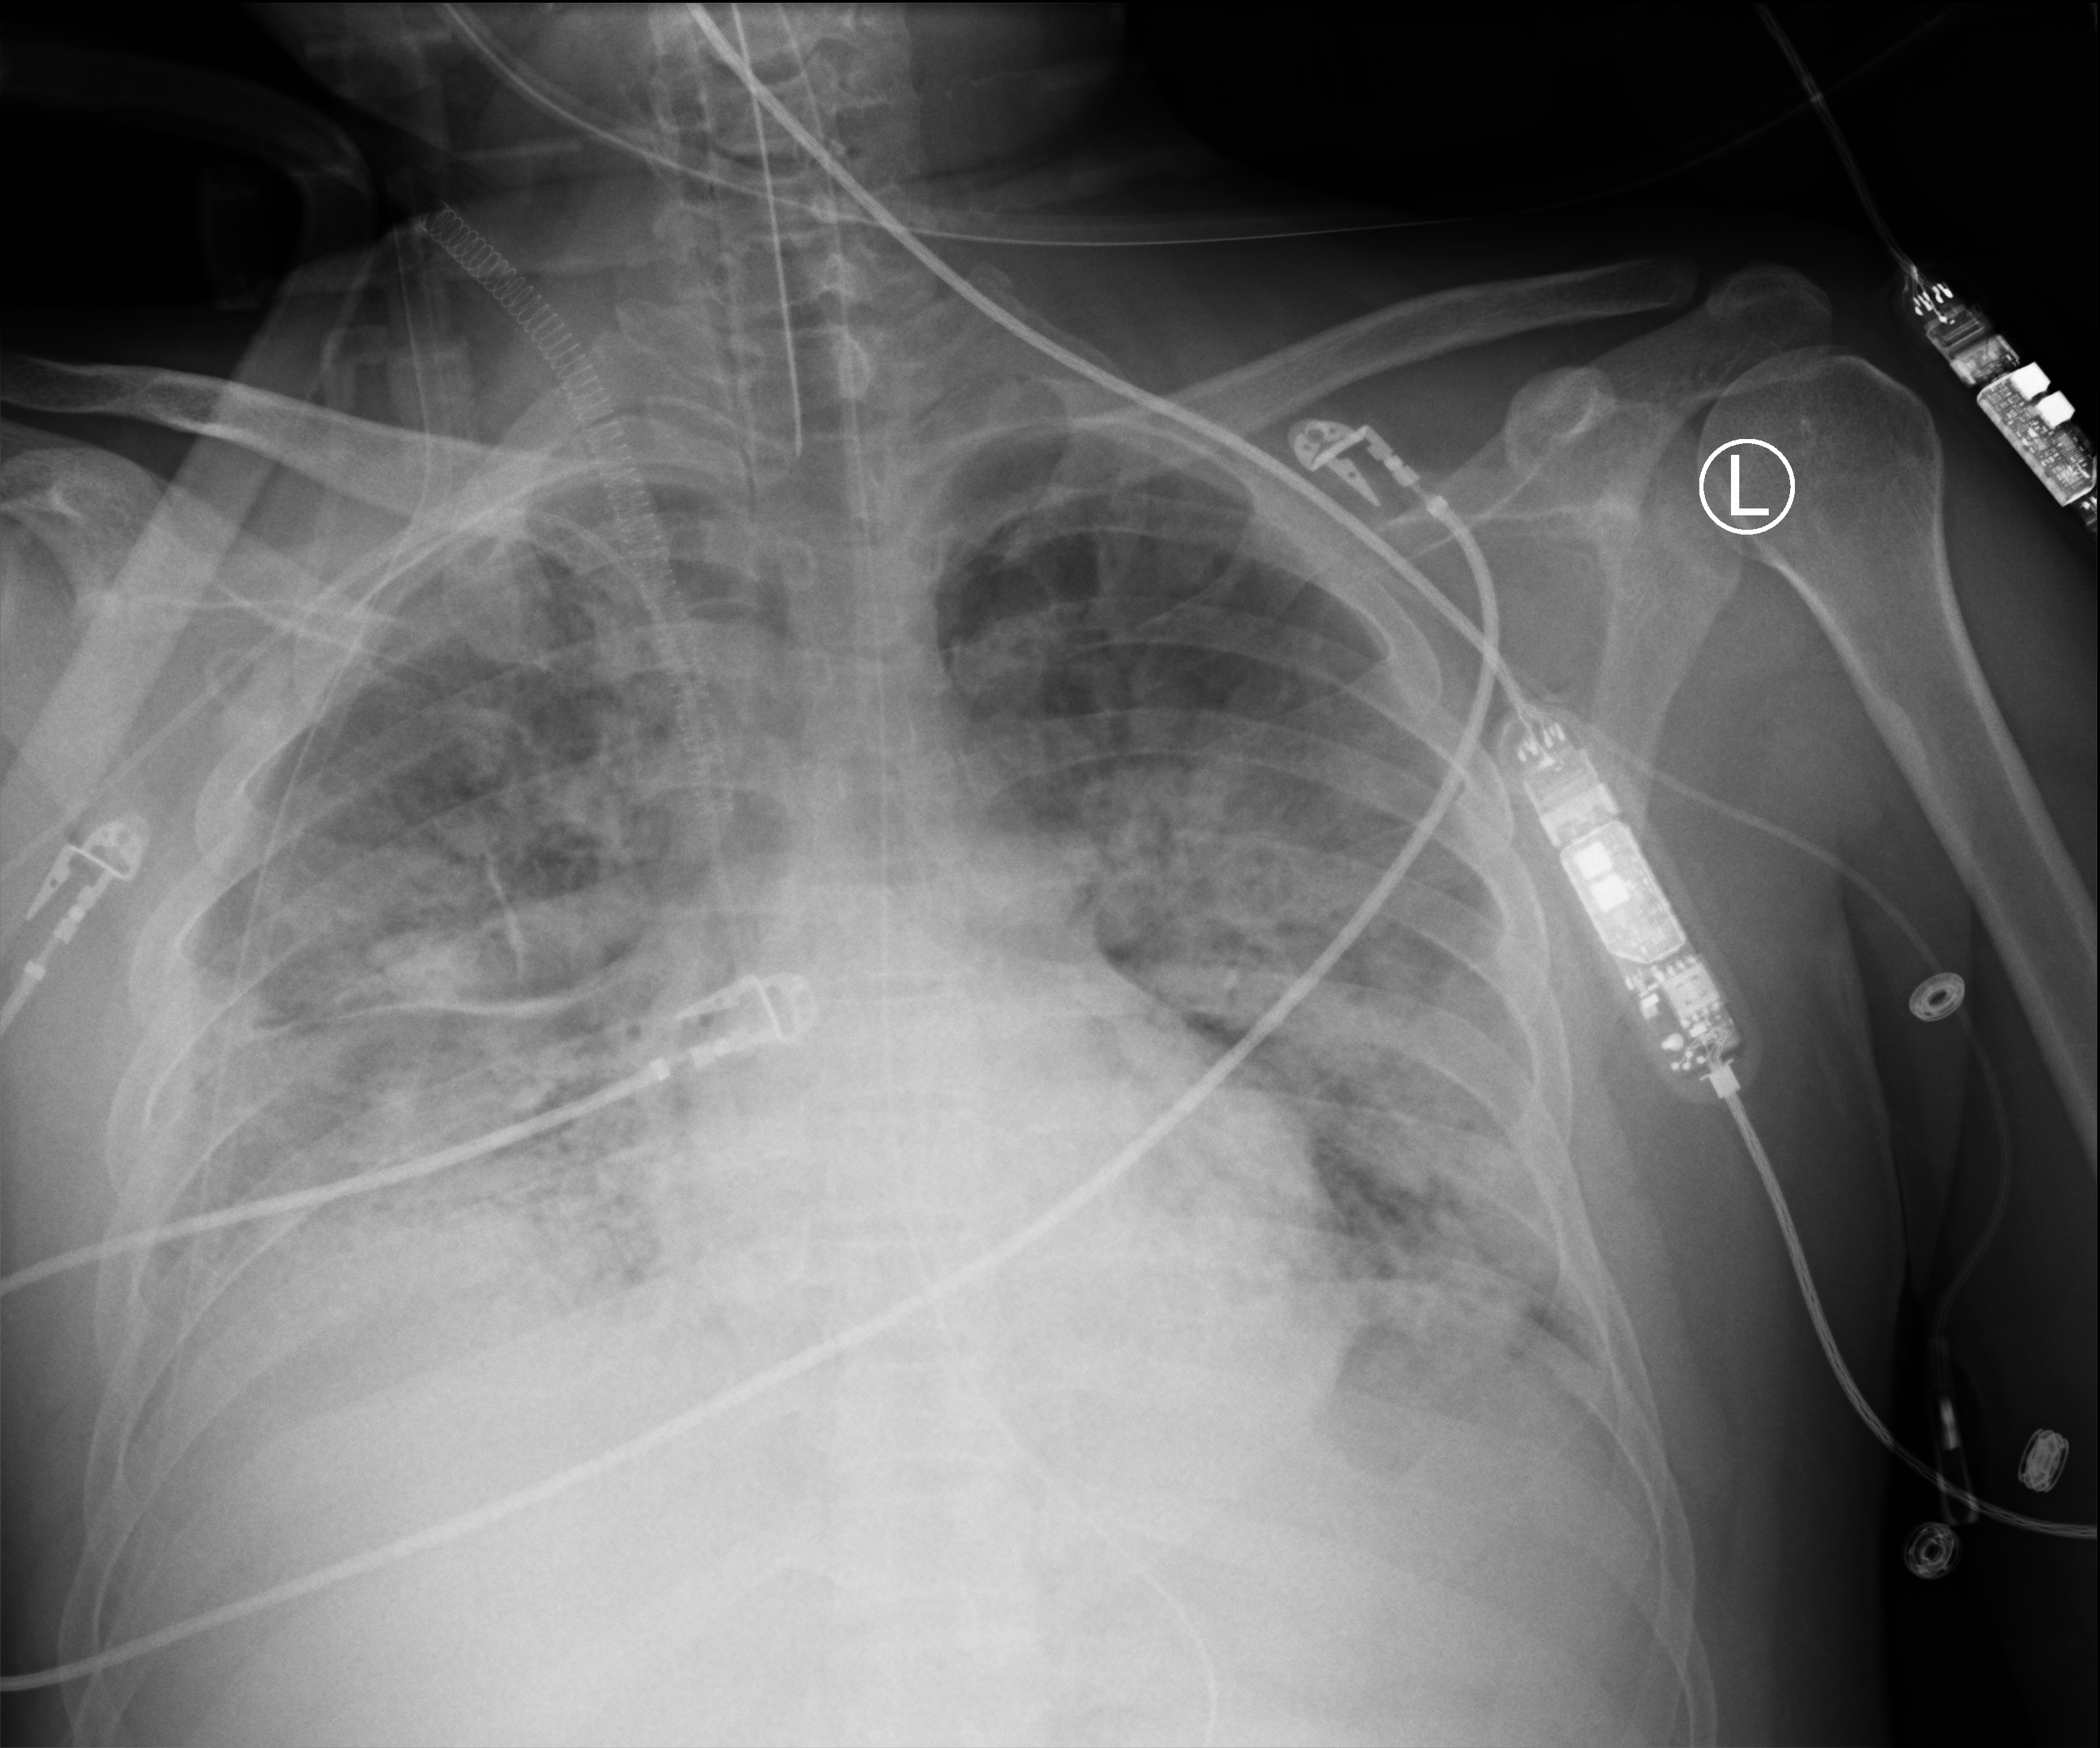
Portable chest radiograph, anteroposterior (AP) projection. Patient hospitalised with COVID-19, aged 18–59 years.
Hospital-stay facts (about this admission, not read from this image; timing relative to this image not recorded): mechanically ventilated during this hospital stay: yes; other chronic lung disease (admission record): no; admitted to intensive care during this hospital stay: yes.